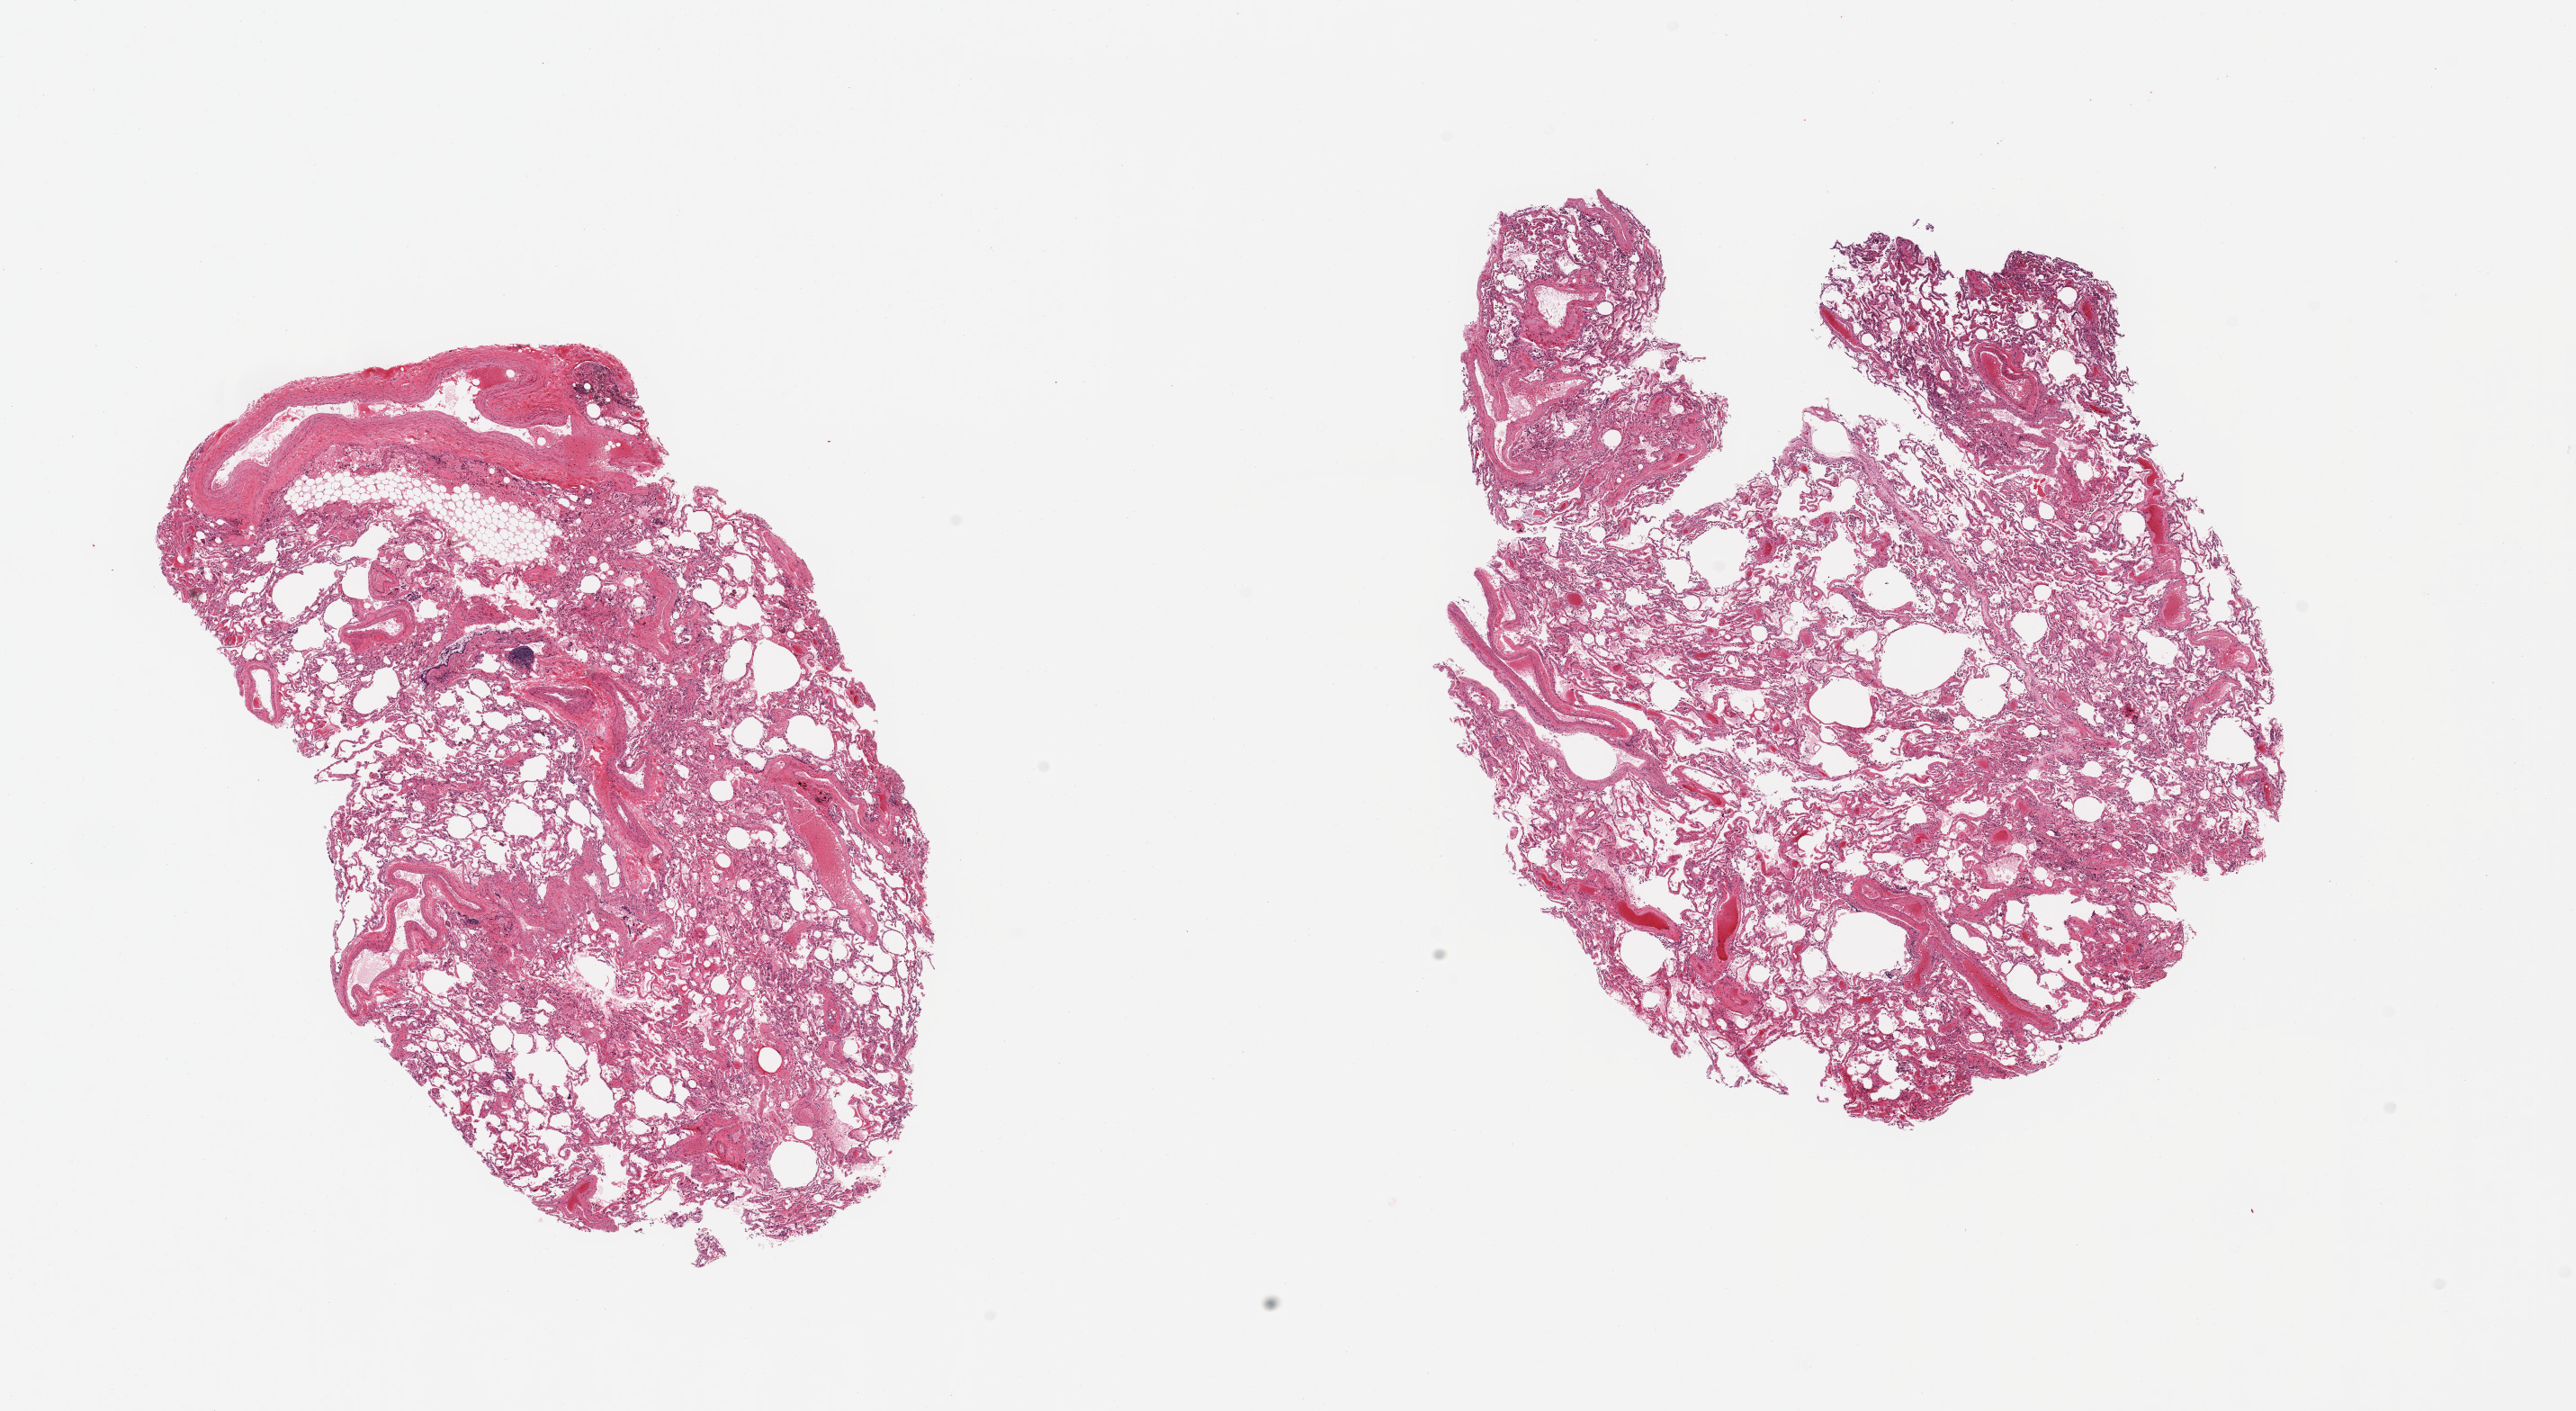
Haematoxylin and eosin whole-slide image — shown as a low-resolution overview of the whole scanned area (about 22.6 x 12.4 mm, from a 20x scan). PAXgene-fixed, paraffin-embedded tissue. Target tissue: lung. Donor tissue sample.
Reviewer comment on this tissue sample: 2 pieces; patchy emphysema & fibrosis; aspiration.